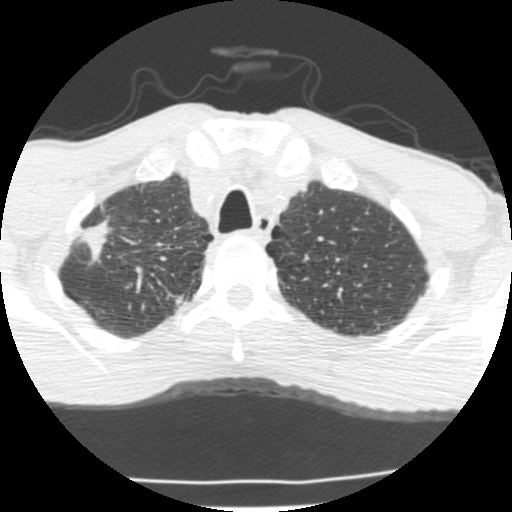
Low-dose screening chest CT, one axial slice; slice 180 of 214 in the series (ordered by position); reconstruction kernel STANDARD; 120 kVp; lung window (W 1500 / L -600 HU); 2.5 mm slice thickness; 512 × 512 image matrix, field of view 283 × 283 mm.
Outlined on this slice (manually delineated by an expert):
- lesion 1 (tumor, upper lobe of right lung): bounding box [x1, y1, x2, y2] px = [80, 218, 112, 265]